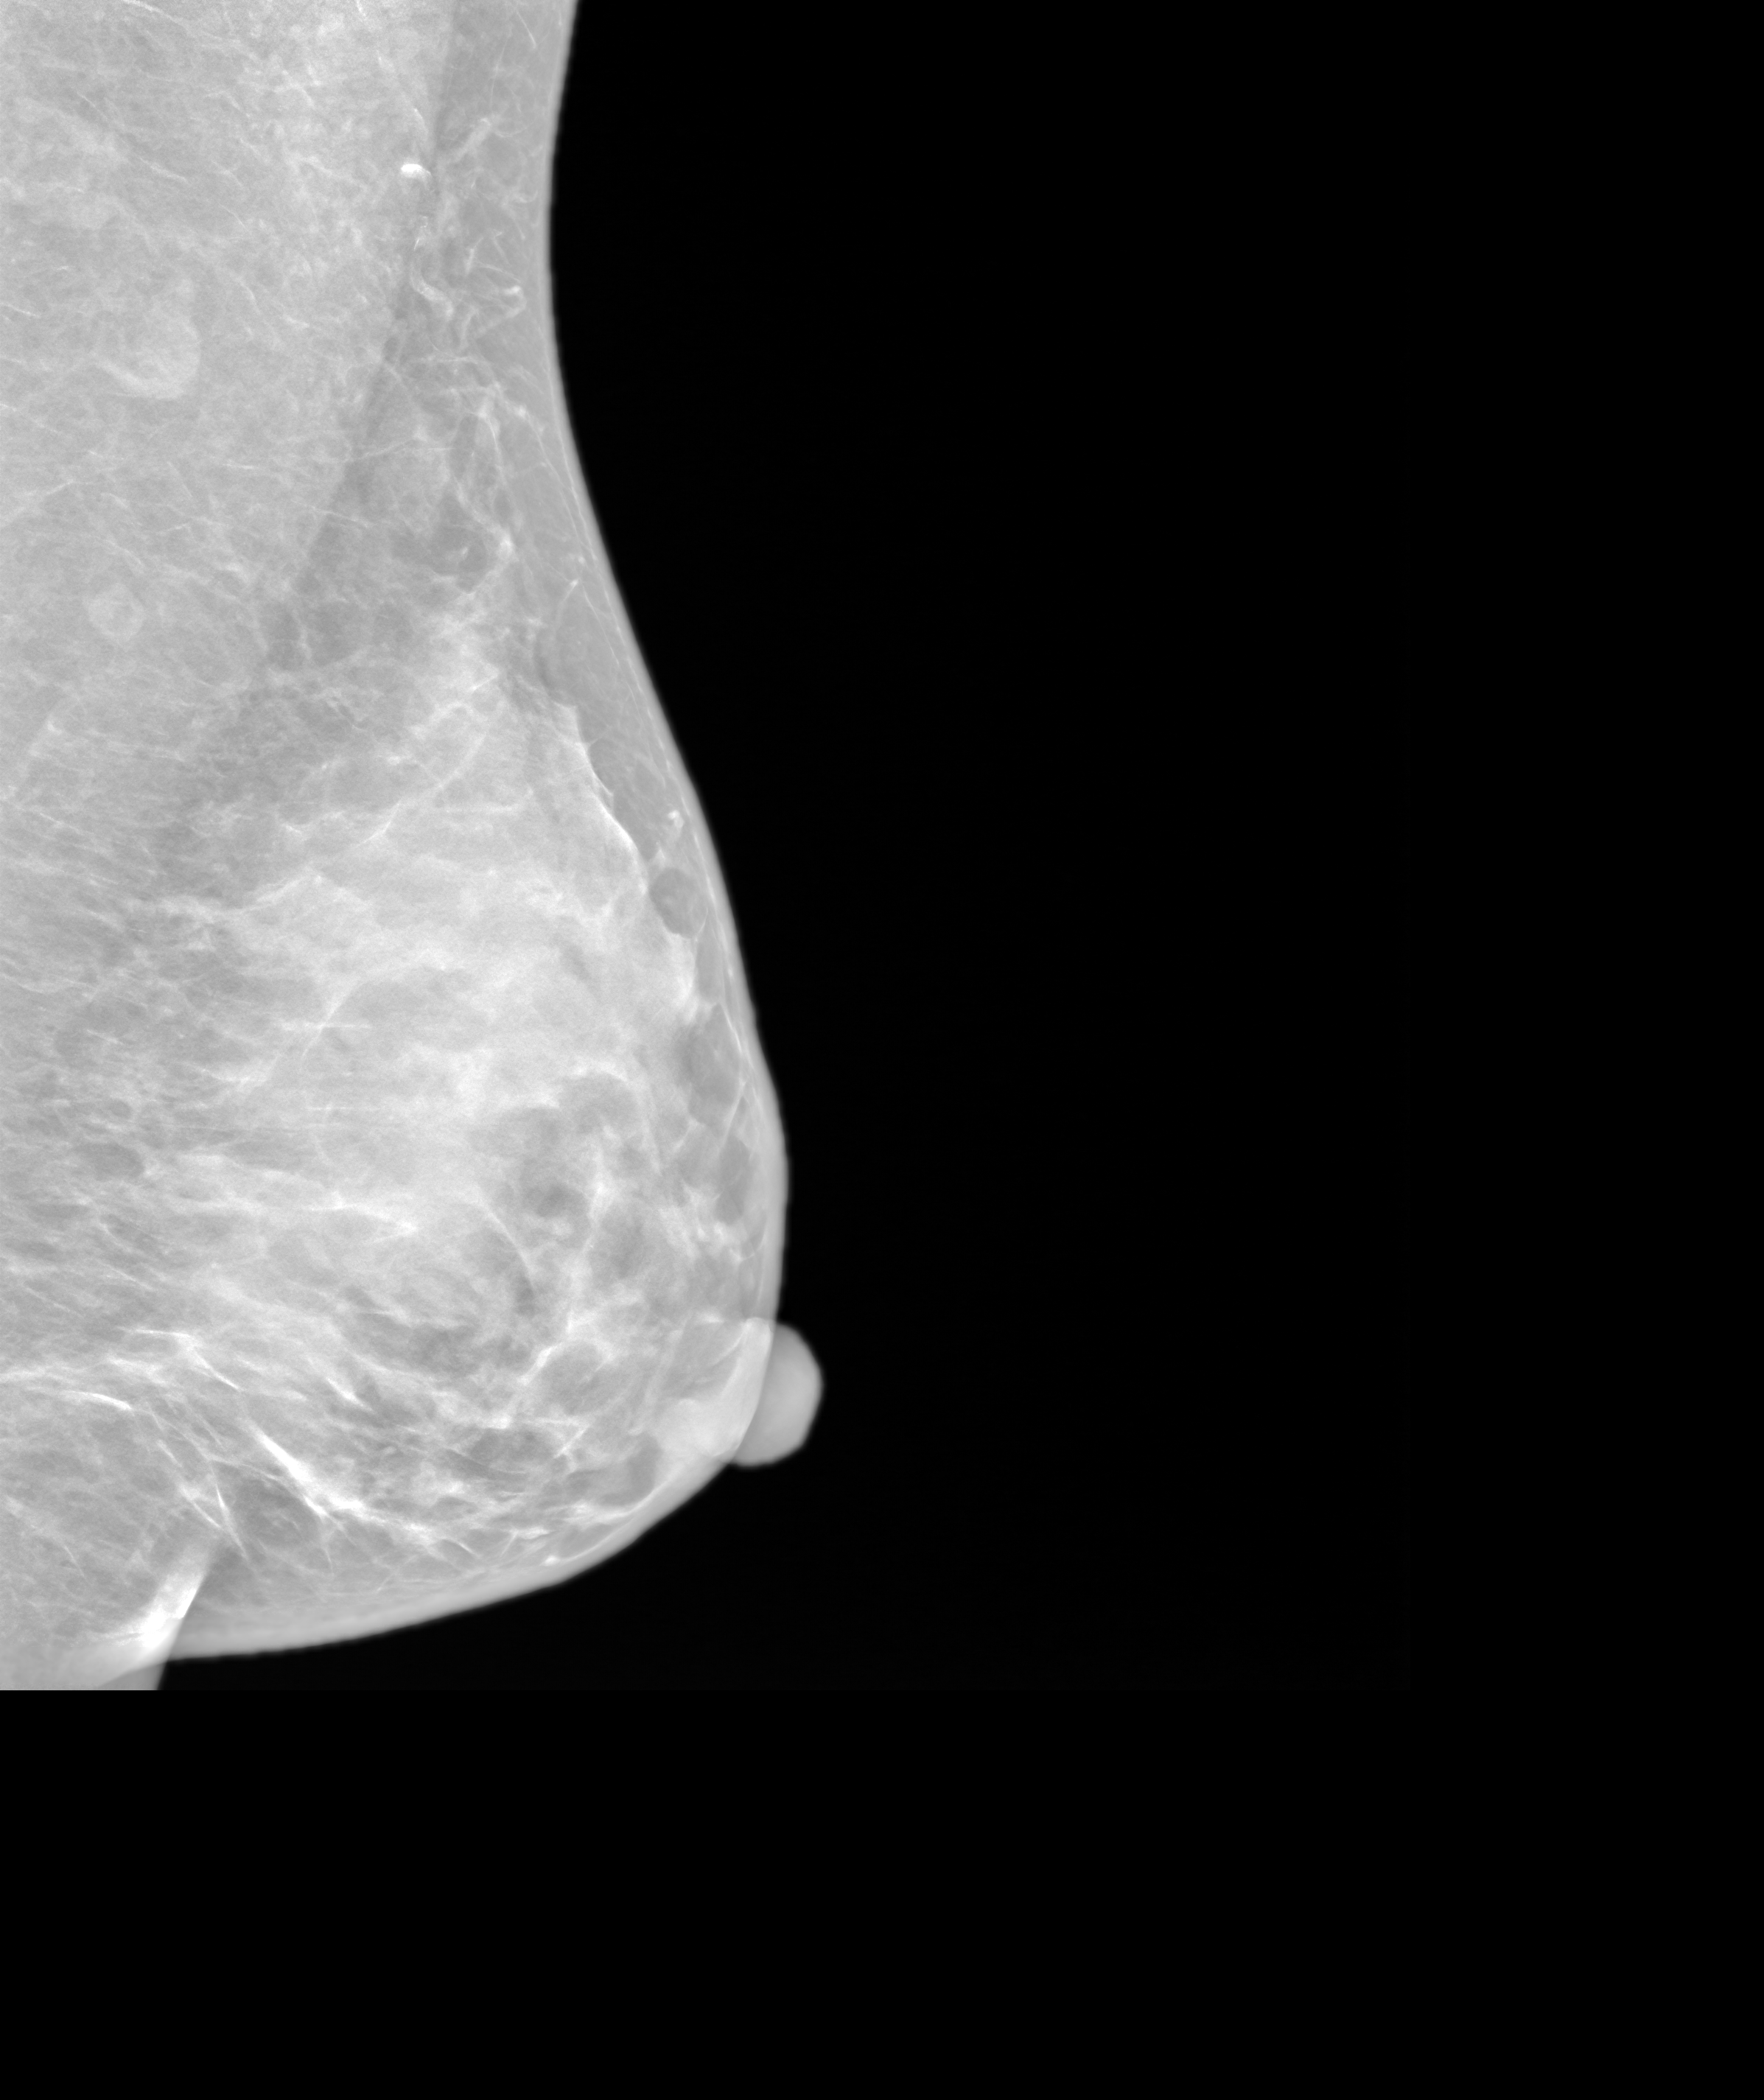
Screening examination. Female patient, age 56 years.
Image type: synthesized 2-D view from tomosynthesis. Breast: left. Projection: mediolateral oblique (MLO) view.